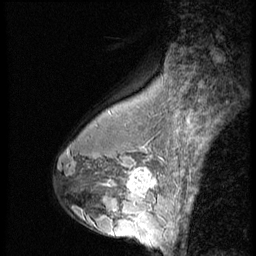
Breast MRI (dynamic contrast-enhanced), one sagittal slice; 3 images stored at this slice position (order not interpretable as contrast timing); 1.5 T; TE 4.2 ms, TR 9 ms; 2.5 mm slice thickness; 256 × 256 image matrix, field of view 180 × 180 mm. Patient: female, 43 years. From the clinical record (not read from this slice): setting: breast cancer imaged before/during neoadjuvant chemotherapy; receptor status: HR-positive, HER2-negative.
Outlined on this slice (semi-automatically segmented with operator editing):
- analysis volume of interest (the breast-tissue region the enhancement analysis was run in; not a lesion): bounding box <120,160,163,207> (left, top, right, bottom; pixels)
- tumour enhancement mask (voxels above the 140 % enhancement threshold inside the analysis volume of interest): <126,168,157,205>